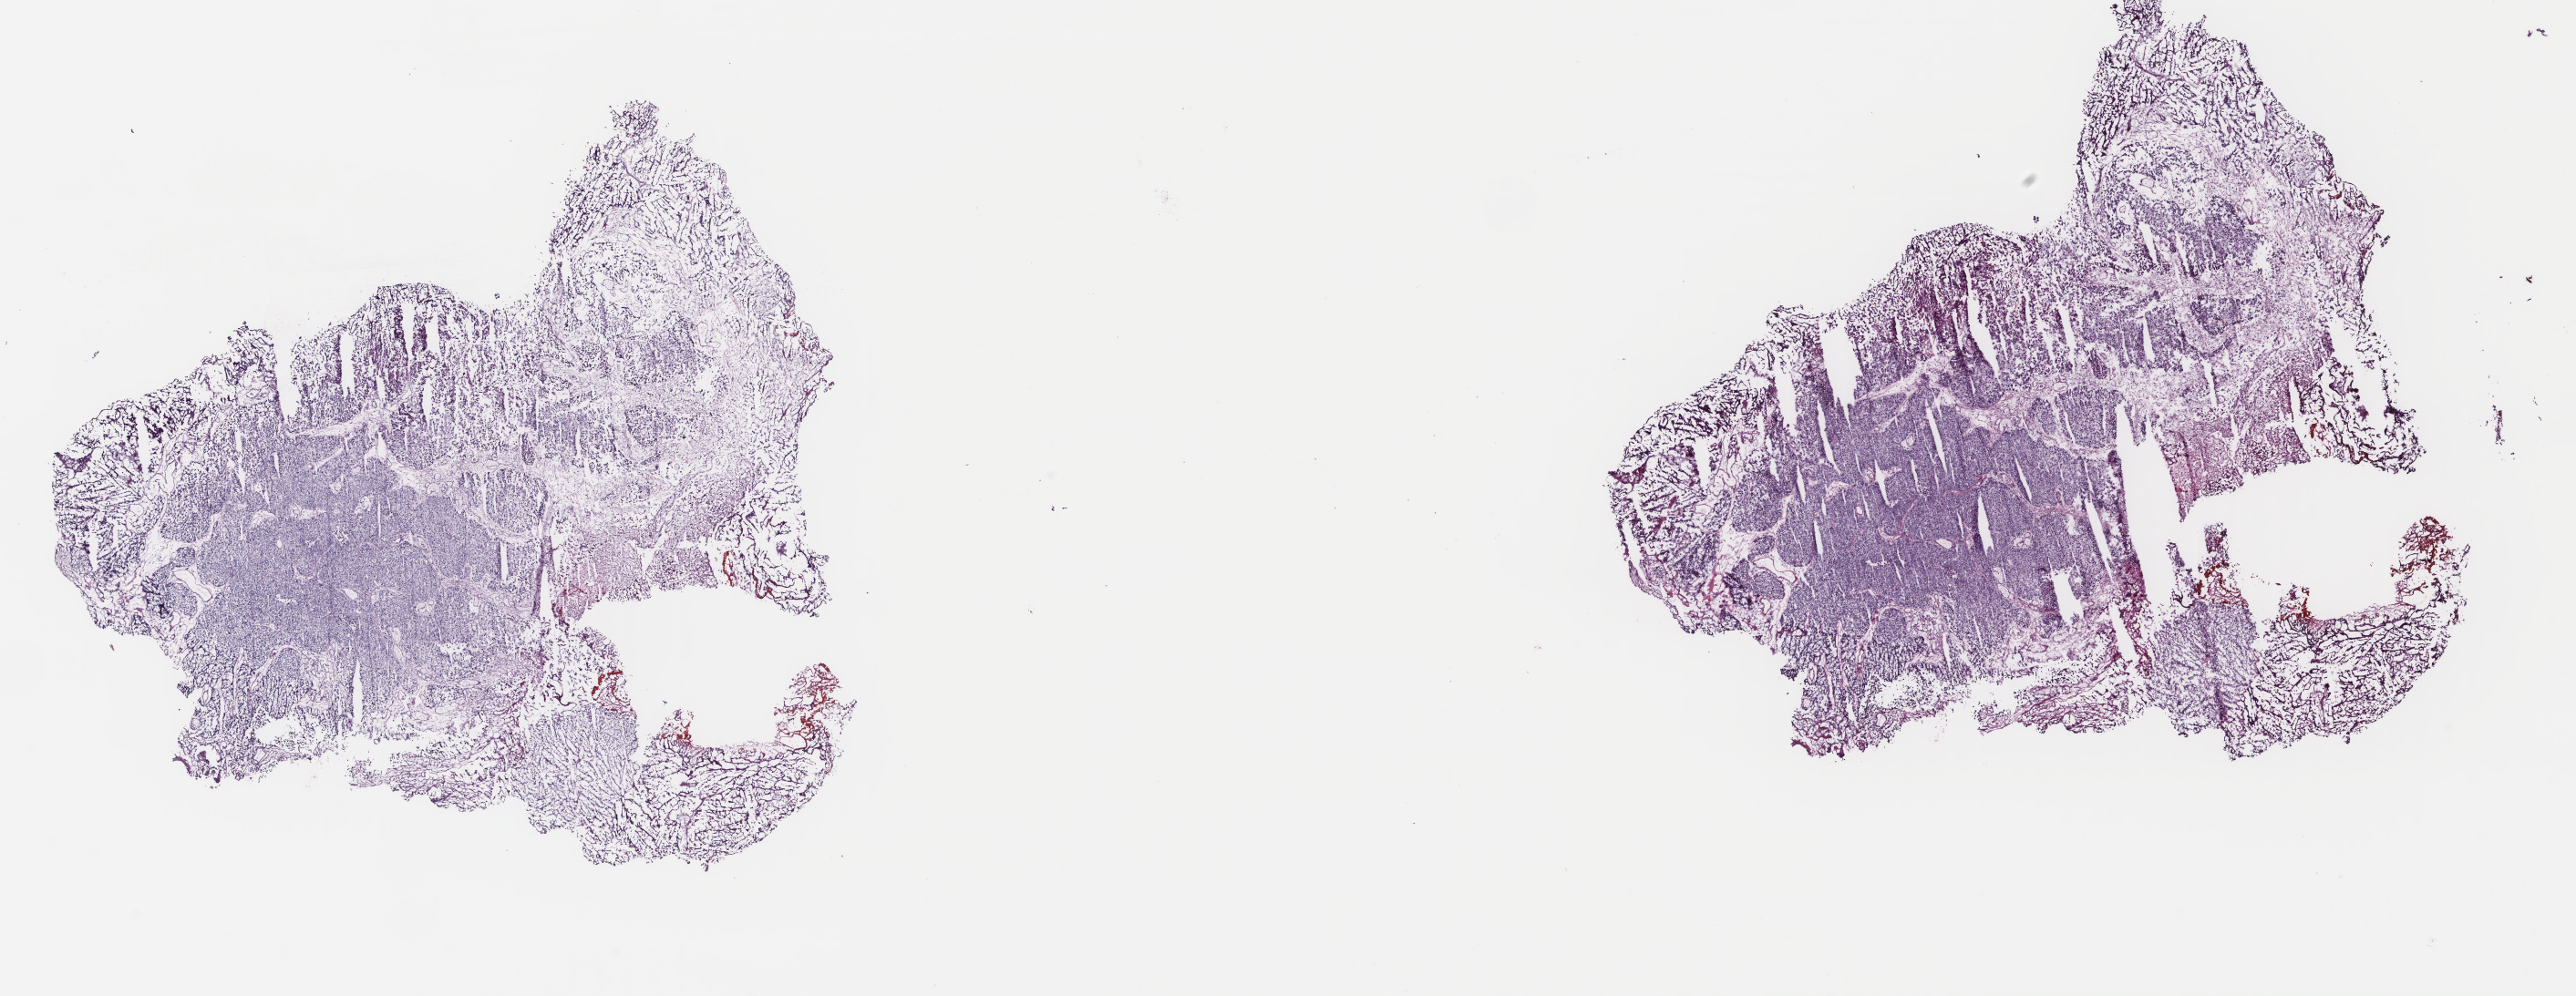
Hematoxylin and eosin (H&E) stained whole-slide image — low-resolution overview of the scanned area, about 22.4 x 8.7 mm (from a 40x scan); frozen section from the top of the tissue portion; primary tumour sample from the bladder. Female patient; age at initial diagnosis 64 years. Histologic grade: high grade. Composition of this section per pathologist review: tumour cells 75%, tumour nuclei 75%, normal cells 0%, stromal cells 18%, necrosis 7%. Infiltration values recorded for this section: lymphocyte infiltration 3%, monocyte infiltration 1%, neutrophil infiltration 1%.
• TNM: NX M1
• histologic diagnosis: Transitional cell carcinoma
• AJCC pathologic stage: IV (7th edition)